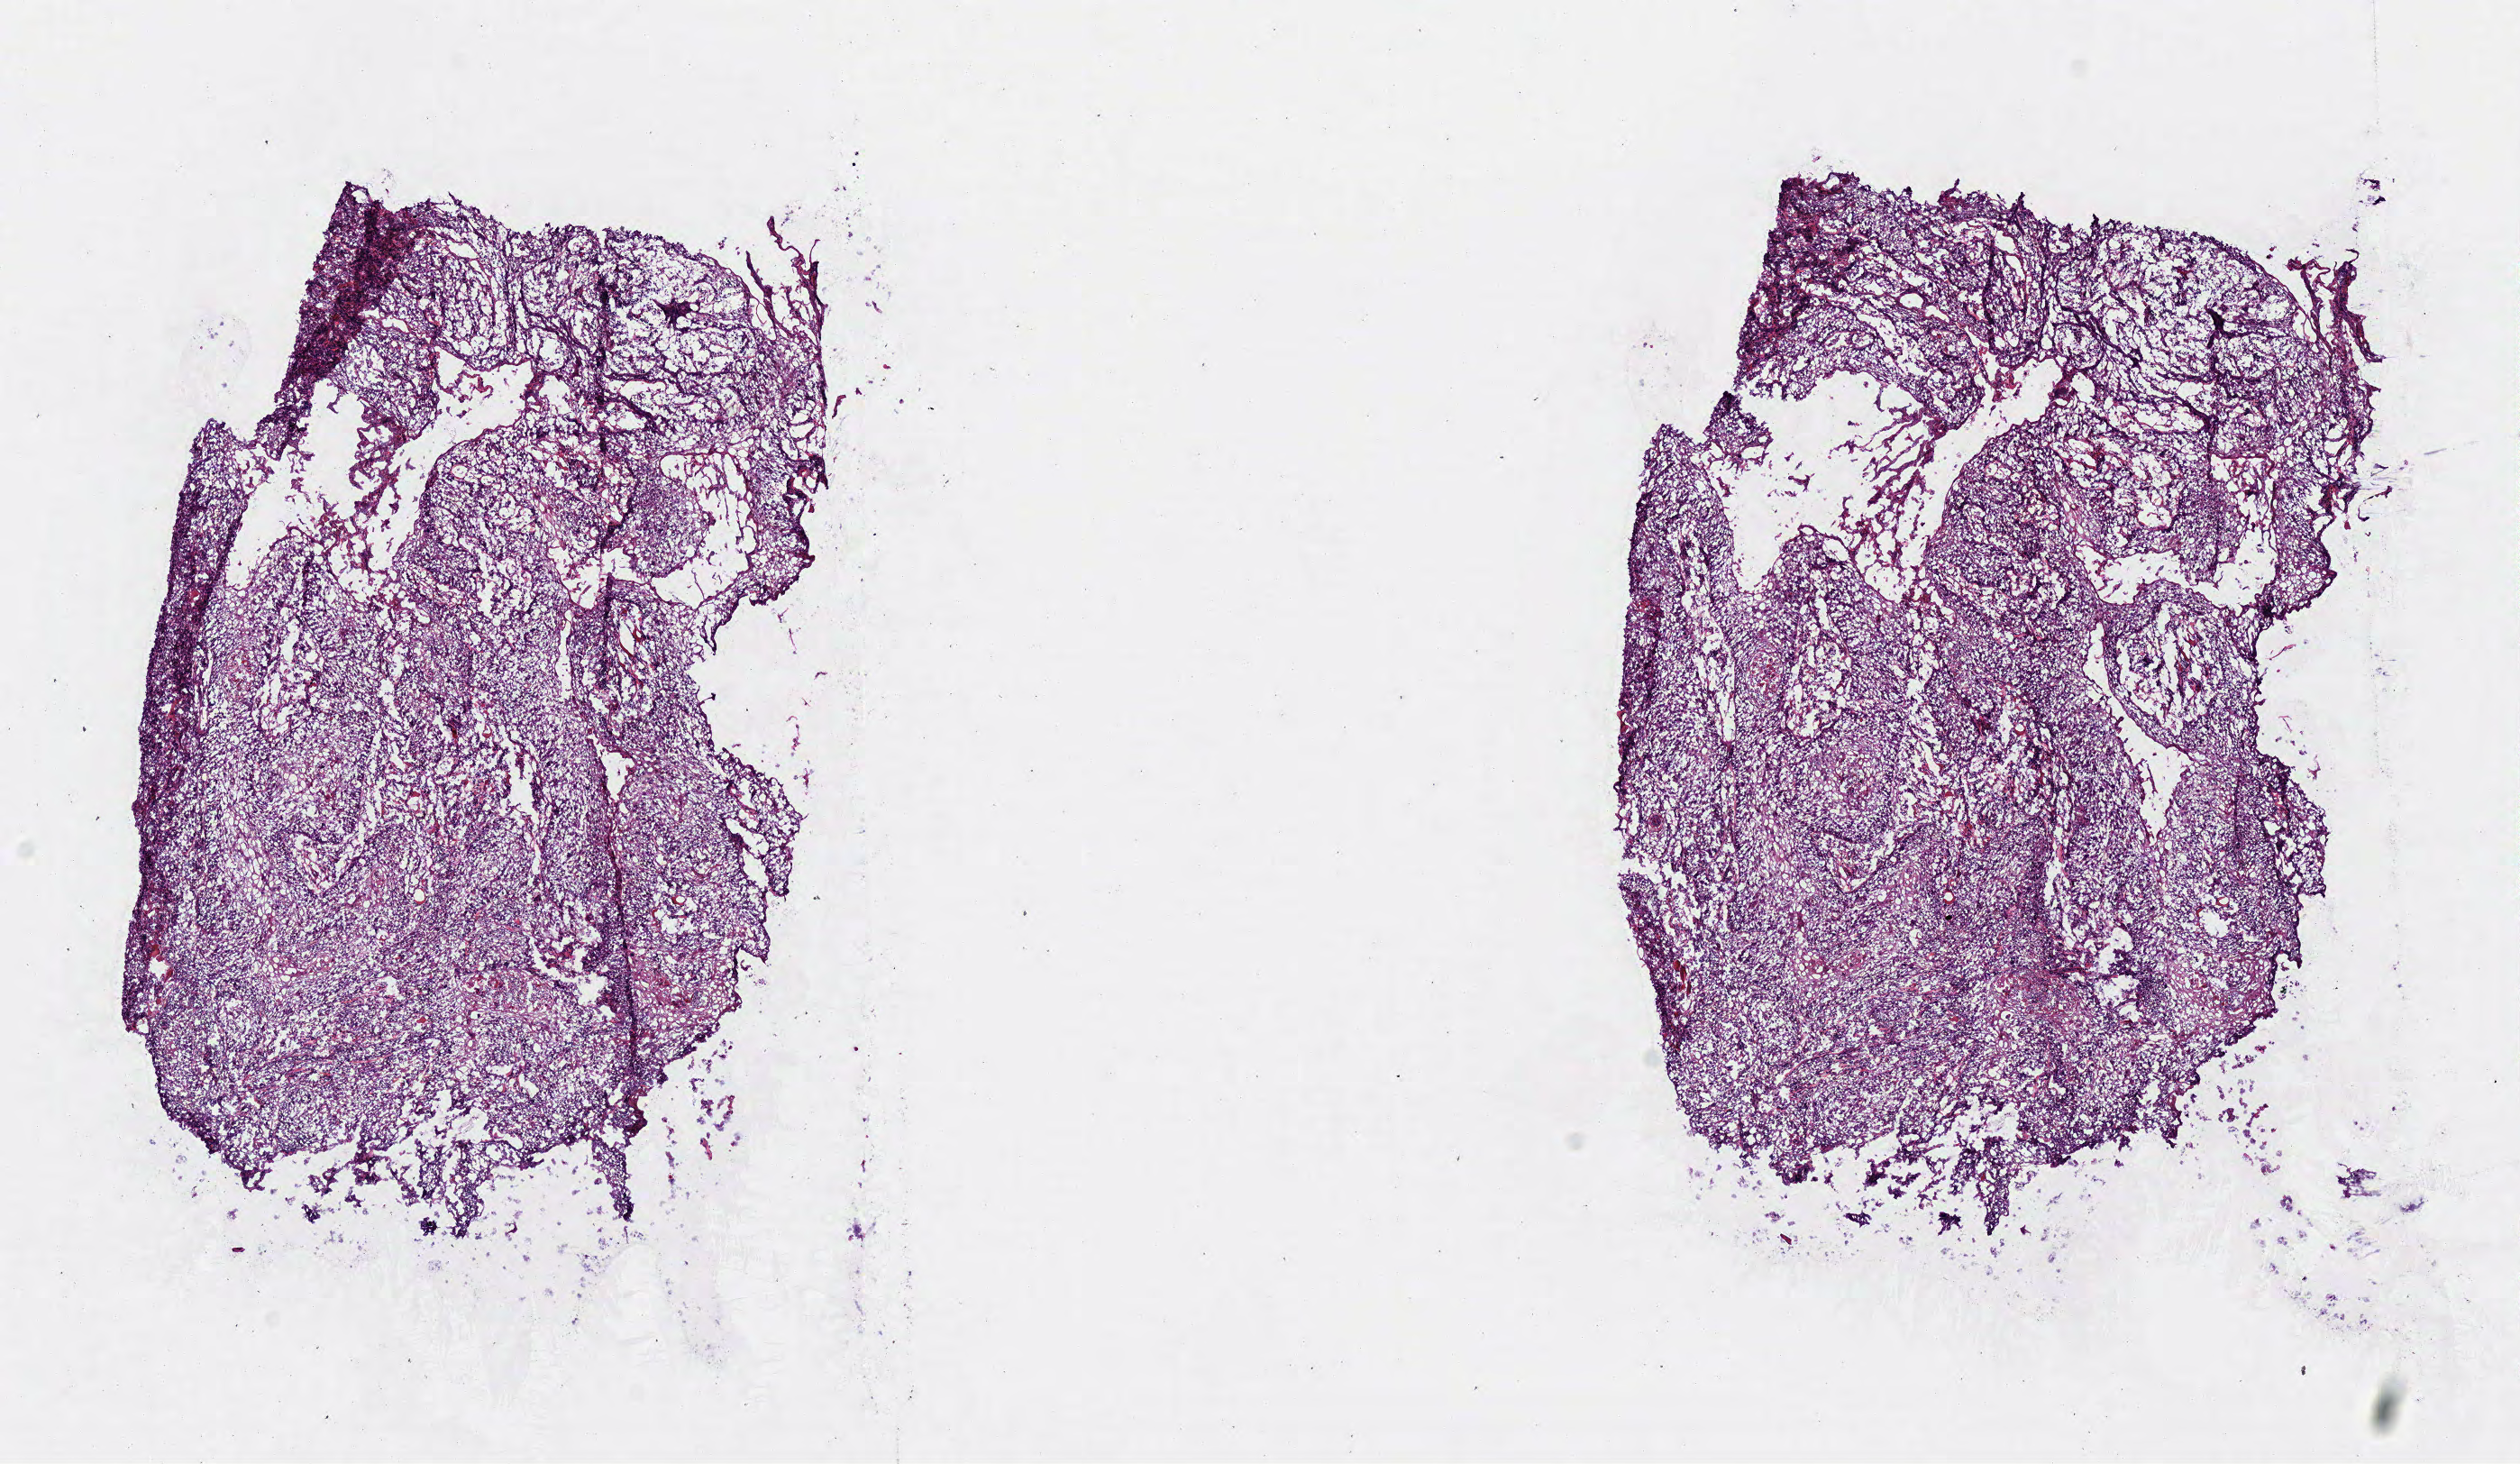
Digitized H&E tissue section (whole slide), shown as a low-resolution overview of the whole scanned area (about 11.0 x 6.4 mm); frozen section; head and neck, primary tumour sample. Male, age 60 years at initial diagnosis.
Histologic diagnosis: Squamous cell carcinoma, NOS (tongue, NOS).